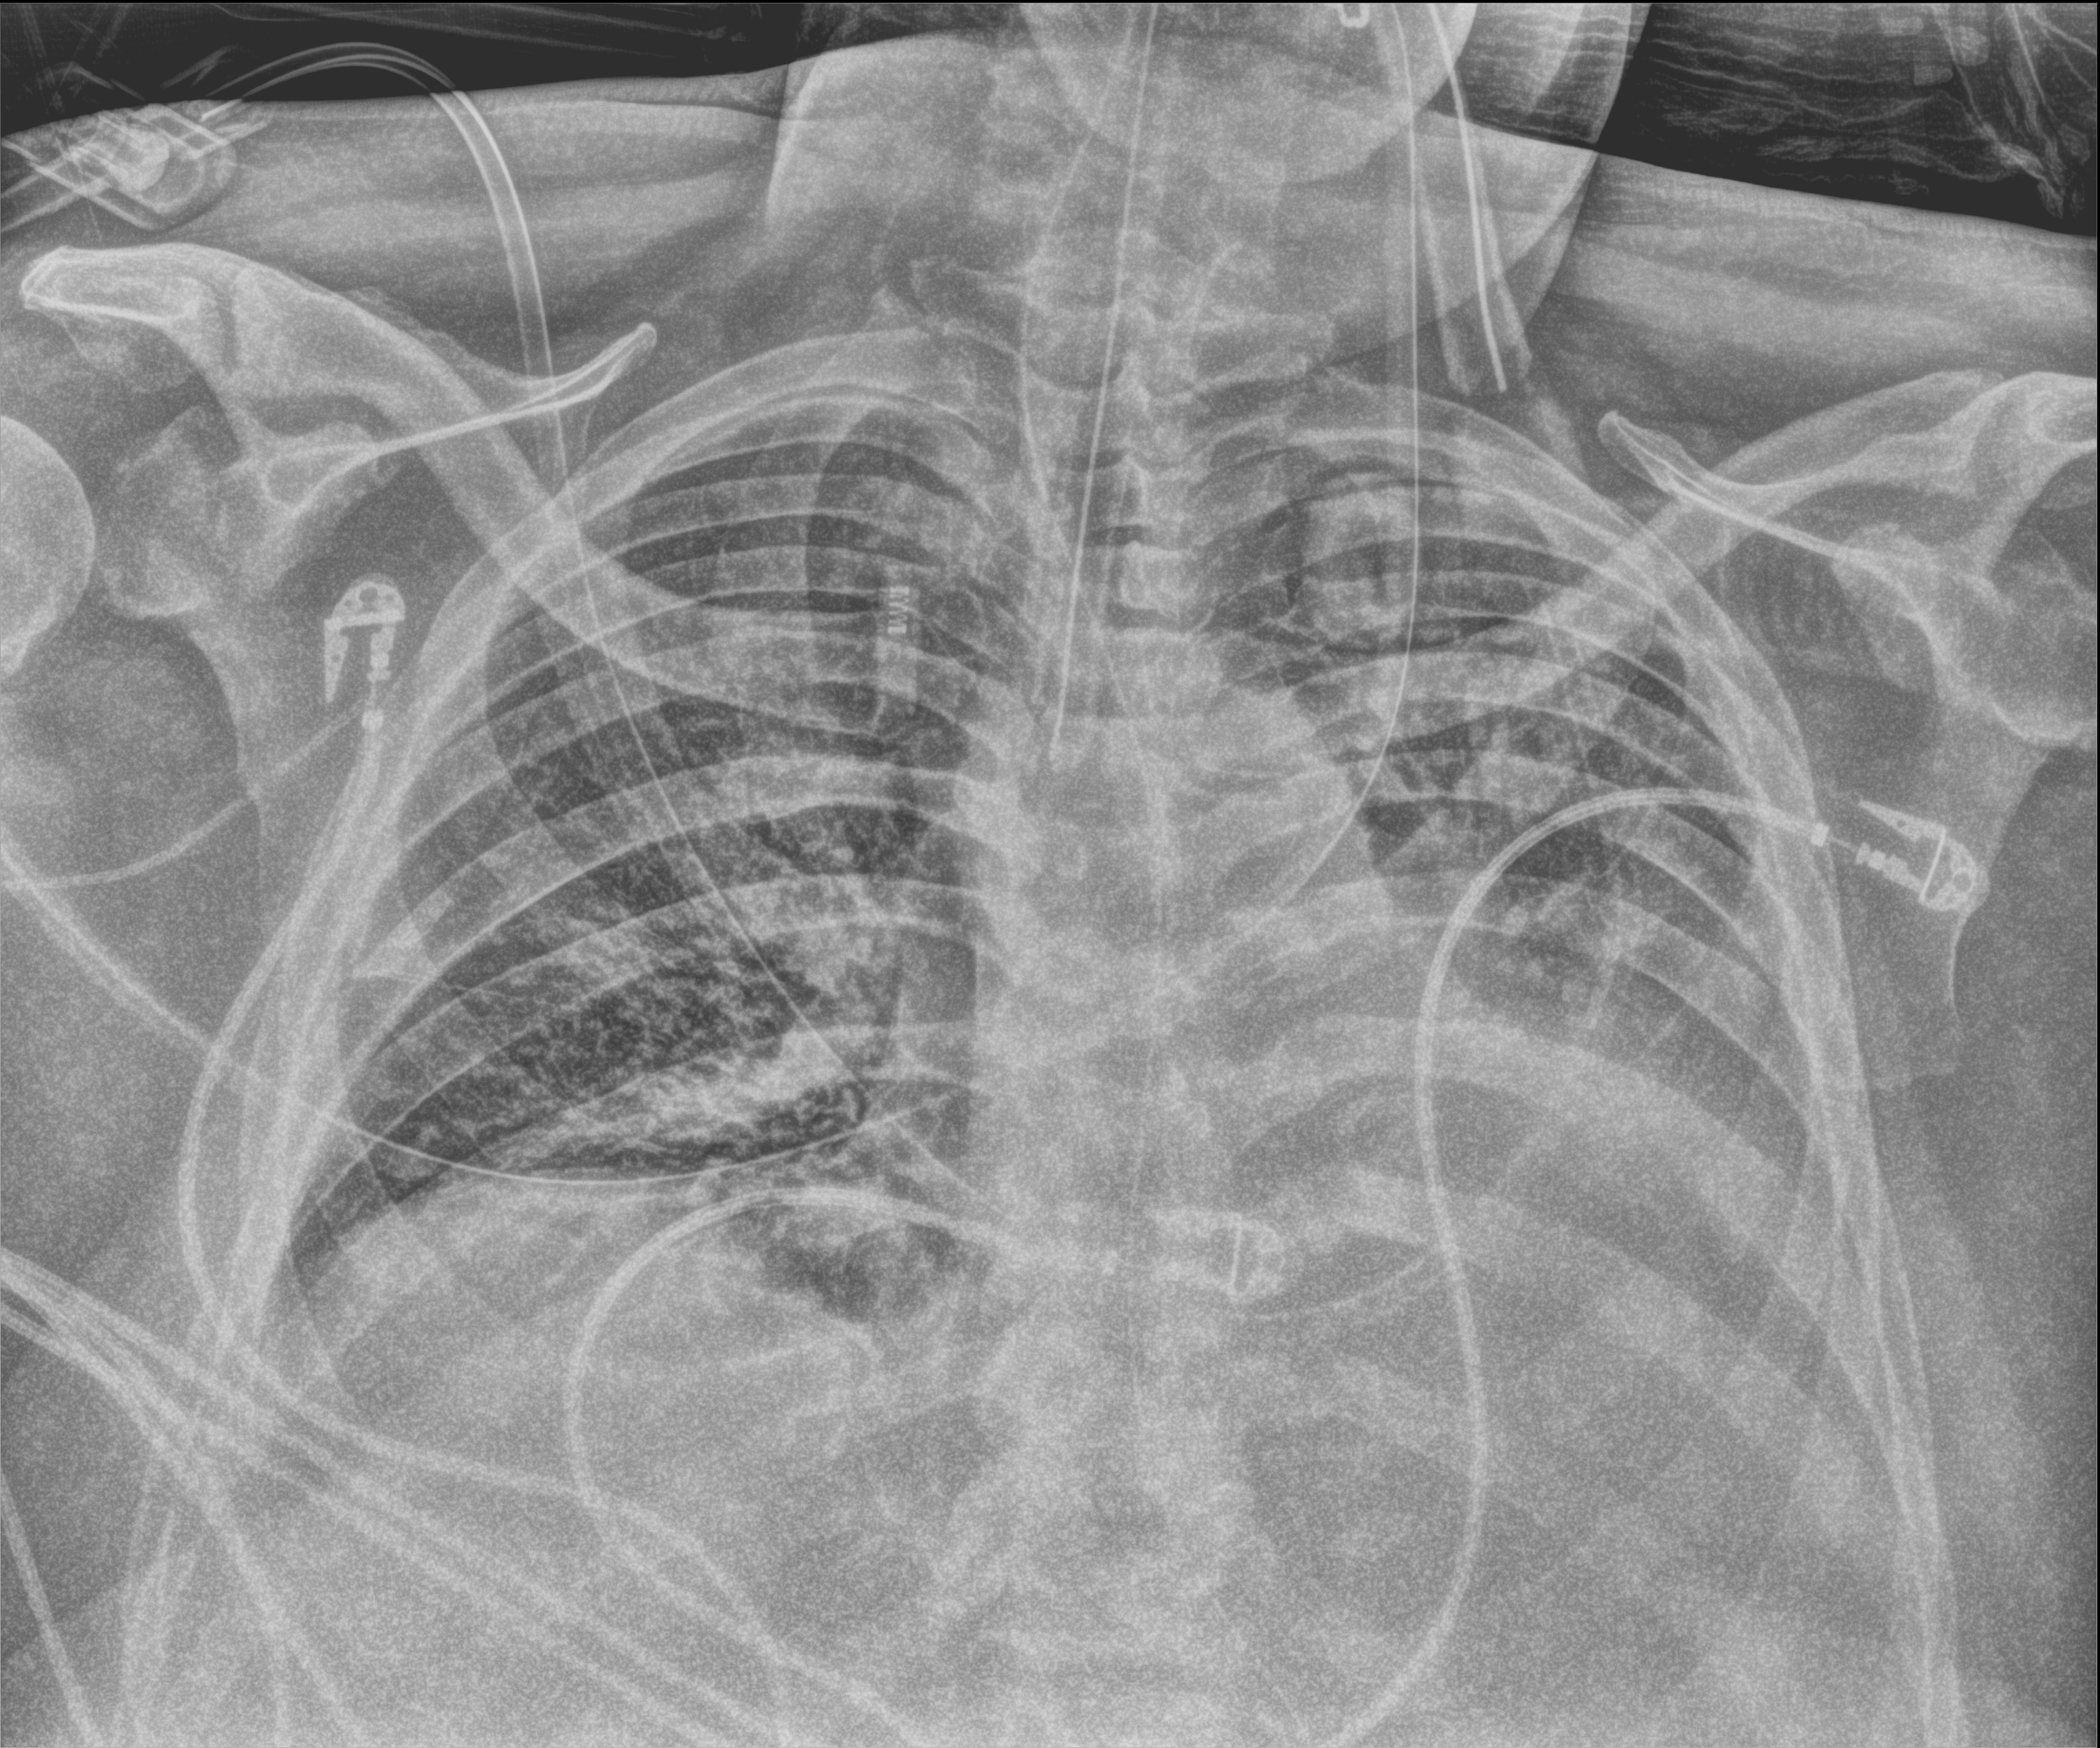
Bedside chest radiograph (computed radiography), anteroposterior (AP) projection. Patient hospitalised with COVID-19; male, aged 60–74 years.
From the hospital-stay record, not from the radiograph (when in the stay this image was taken is not recorded):
- admitted to intensive care during this hospital stay: yes
- other chronic lung disease (admission record): no